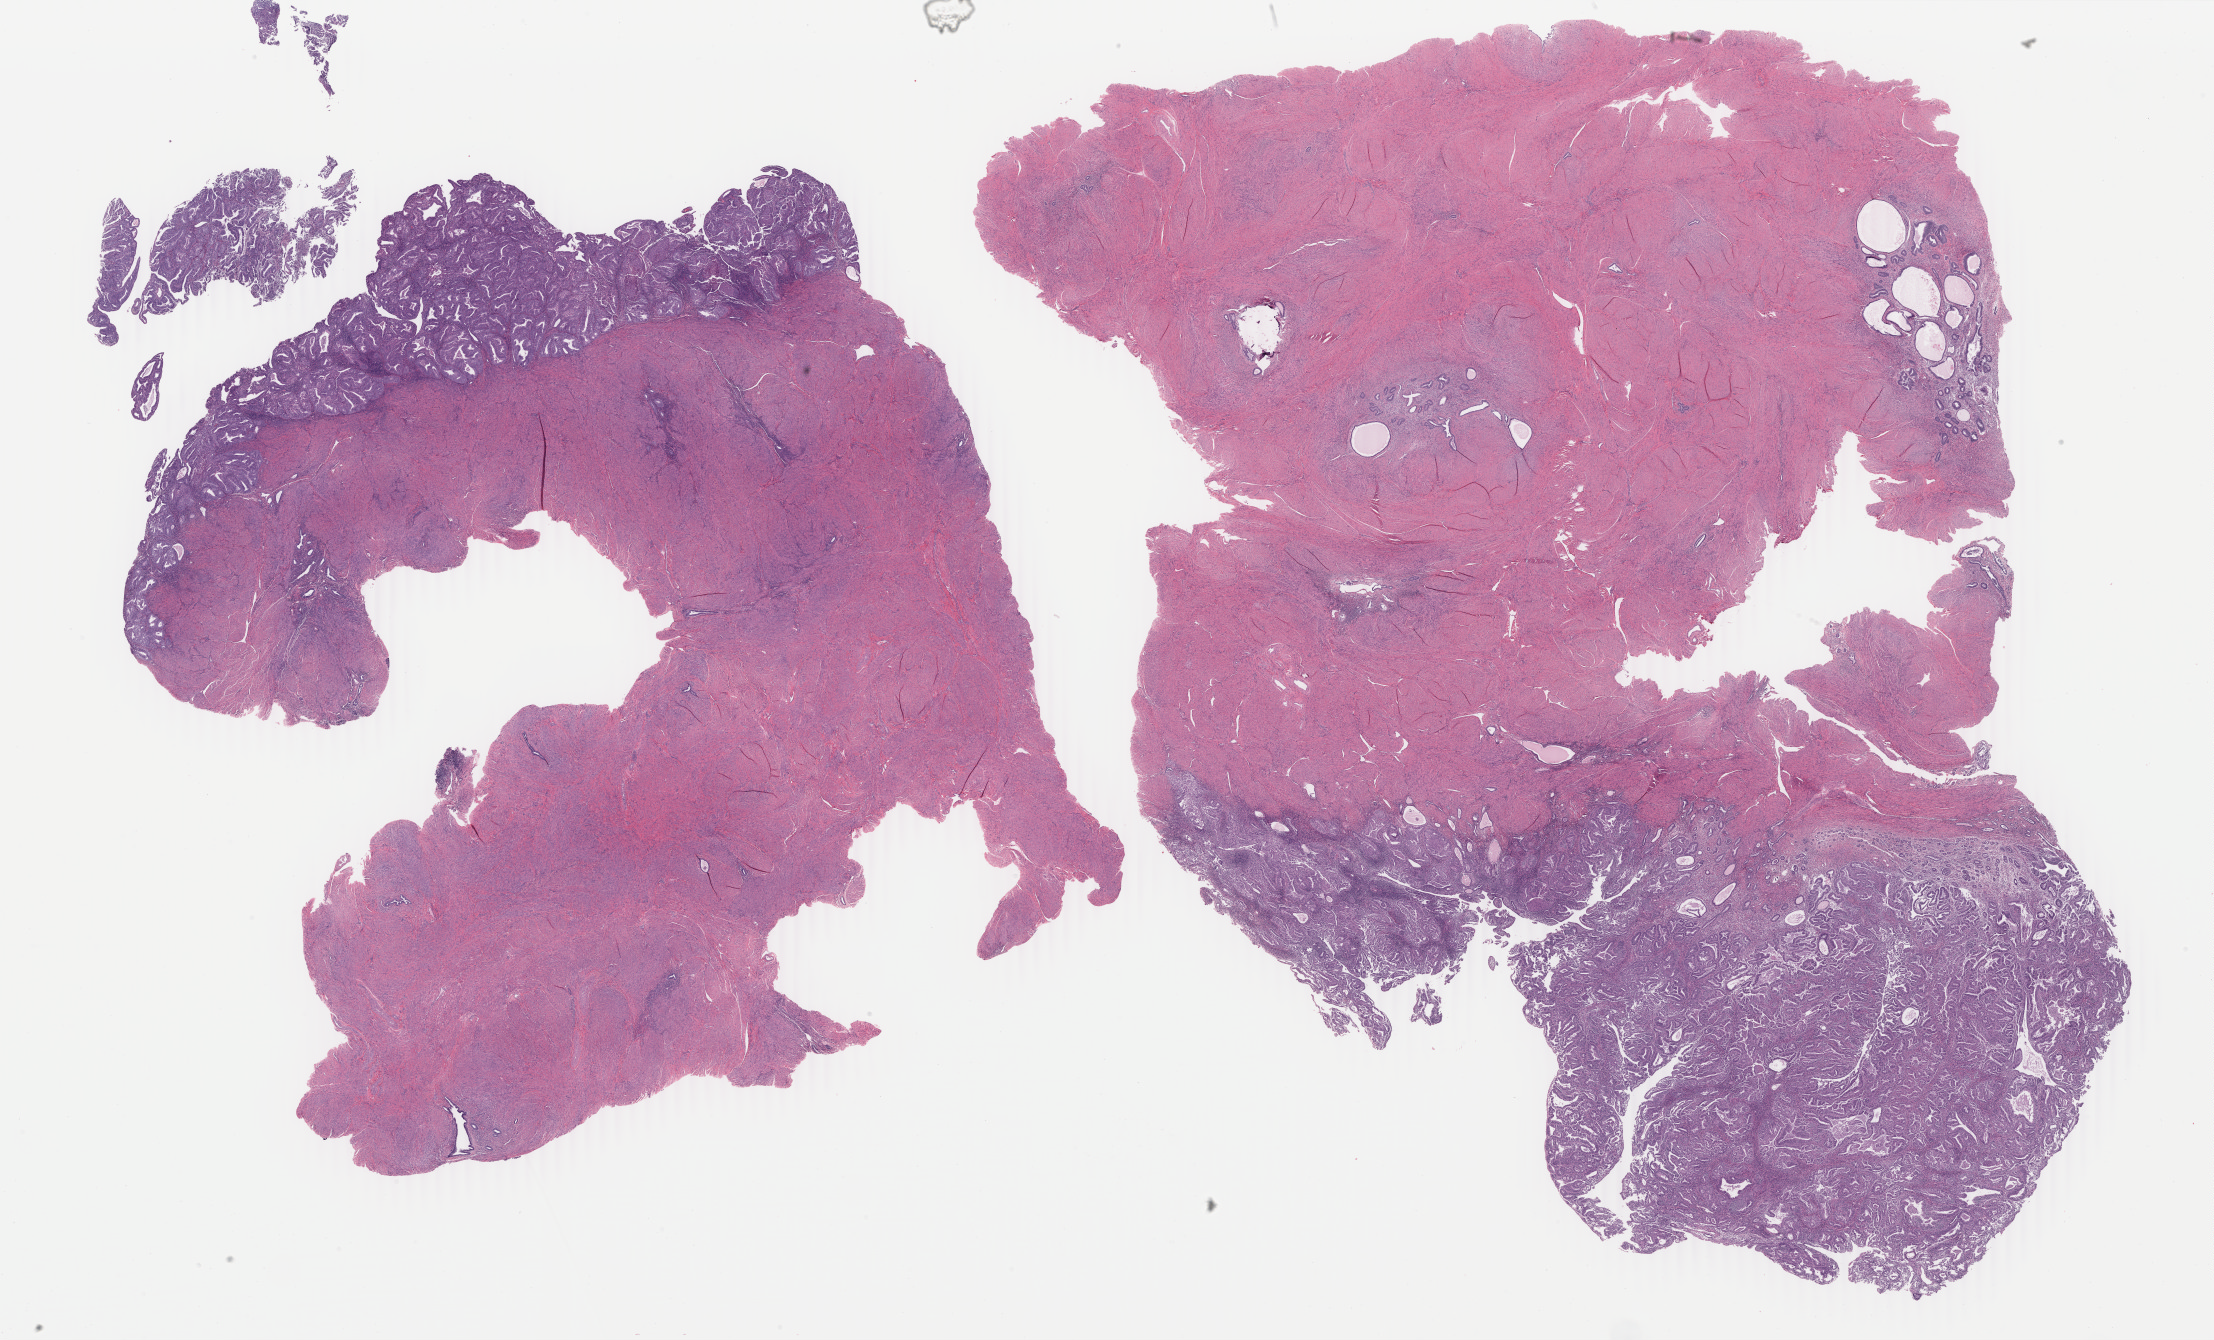
Whole-slide histology image, H&E-stained, shown as a low-resolution overview of the whole scanned area (about 35.2 x 21.3 mm, slide scanned at 40x), FFPE section, primary tumour sample from the uterus. Female patient; age at initial diagnosis 46 years. Histologic grade: G2 (moderately differentiated).
• FIGO stage: IA
• histologic diagnosis: Endometrioid adenocarcinoma, NOS (endometrium)